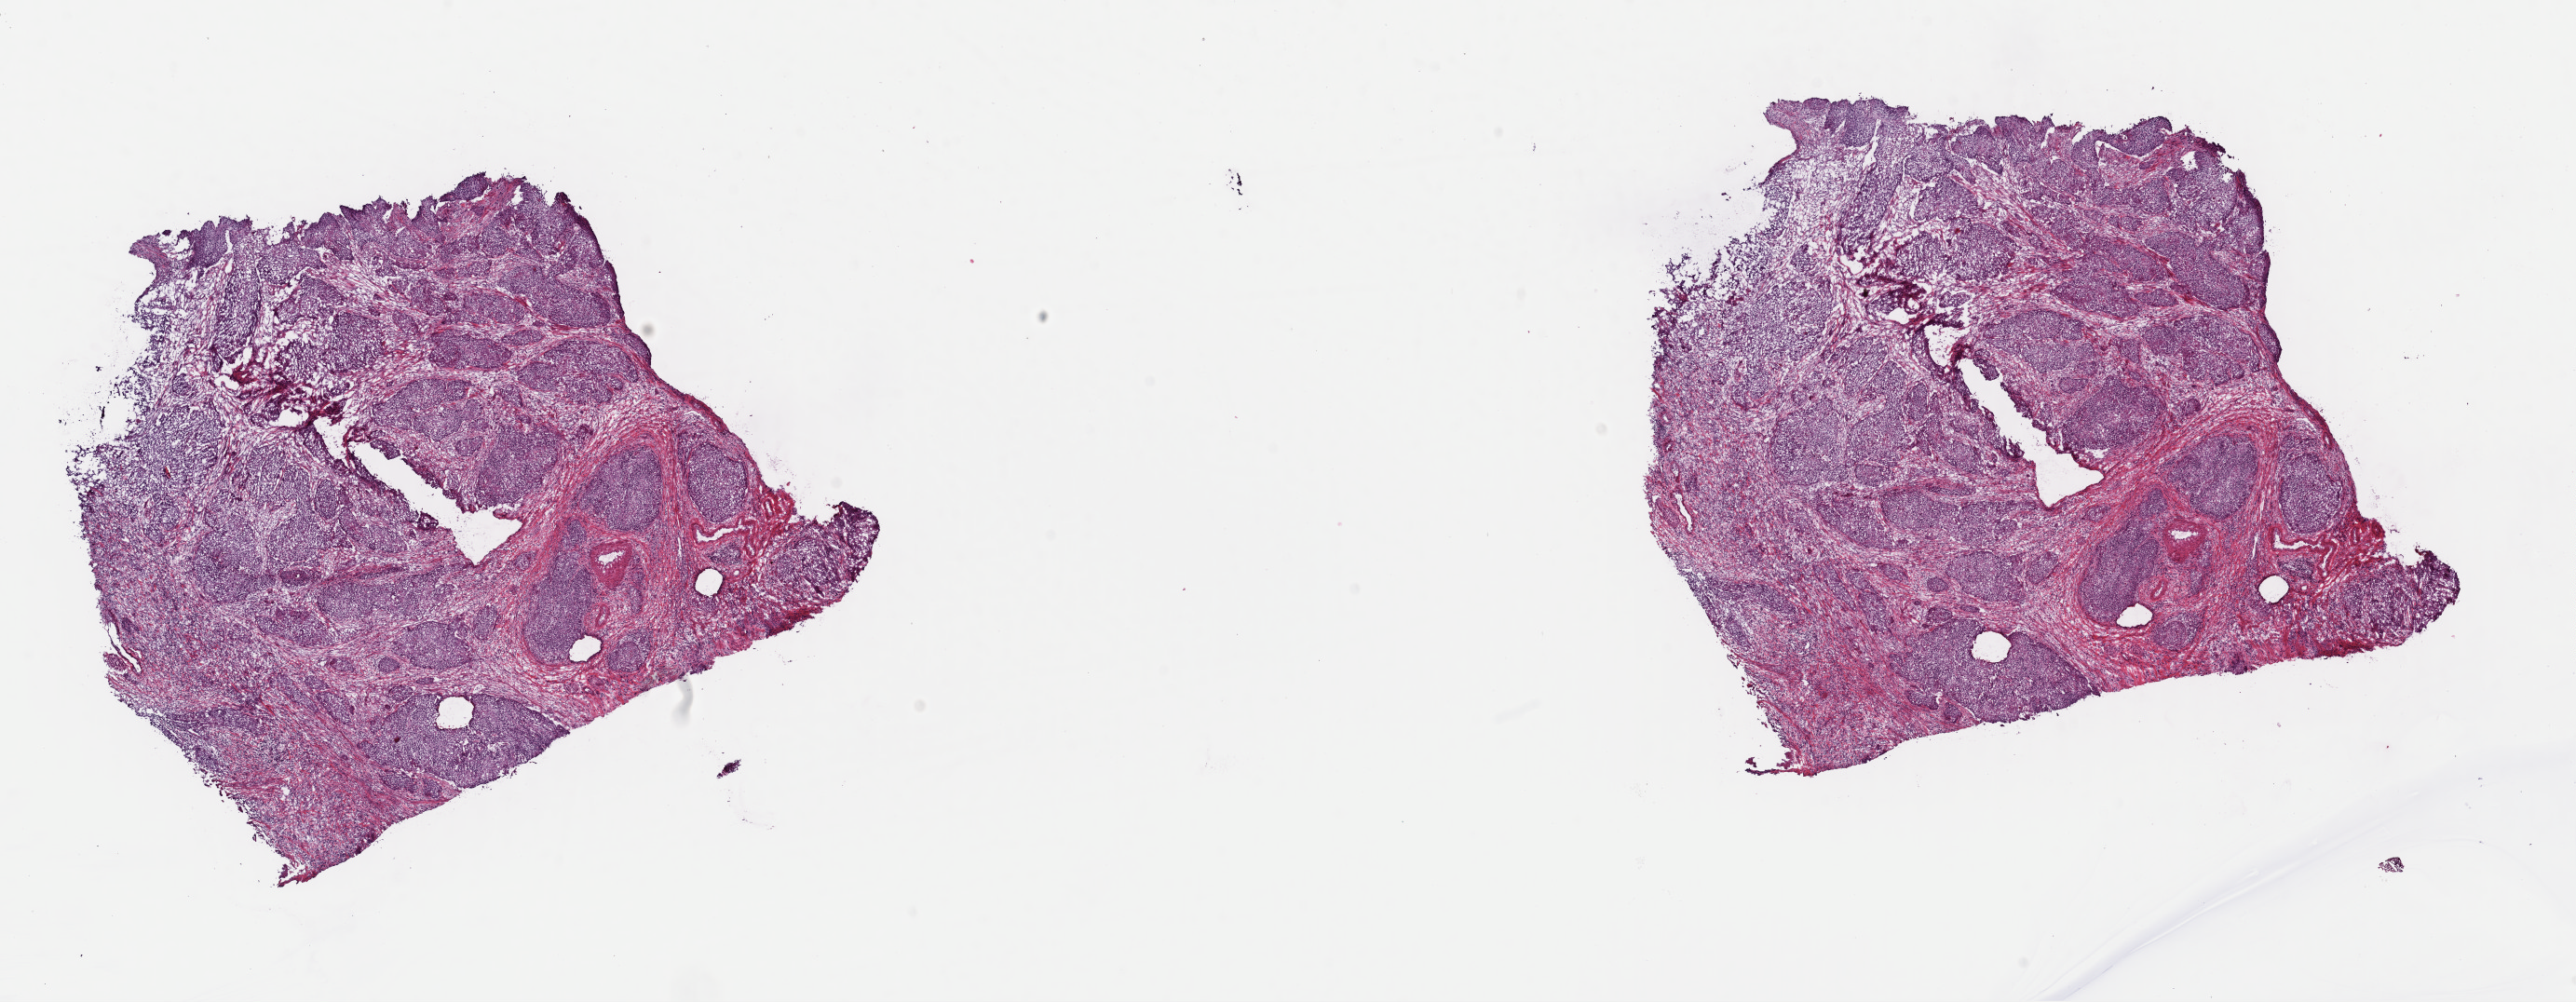
Digitized Hematoxylin and eosin (H&E) stained tissue section (whole slide) — shown as a low-resolution overview of the whole scanned area (about 21.9 x 8.5 mm). Frozen section from the top of the tissue portion. Cervix, primary tumour sample. Female patient; age at initial diagnosis 68 years. Histologic grade: G1 (well differentiated). Slide review estimates, as recorded: tumour cells 95%, tumour nuclei 85%, normal cells 5%, stromal cells 0%, necrosis 0%. Inflammatory infiltration, as recorded: lymphocyte infiltration 7%, monocyte infiltration 0%, neutrophil infiltration 0%.
FIGO stage: IB. Histologic diagnosis: Squamous cell carcinoma, NOS (cervix uteri). Lymph nodes positive (case pathology): 0 of 9 examined.